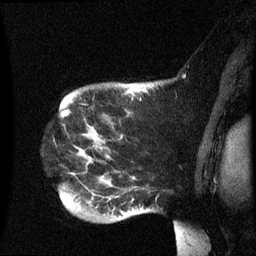
Breast MRI (dynamic contrast-enhanced), one sagittal slice; position 52 of 60 along the scan axis; dynamic contrast-enhanced series, image 2 of 3 at this slice position (ordered by acquisition); 1.5 T; TE 4.2 ms, TR 8.4 ms; 256 × 256 image matrix, field of view 220 × 220 mm. Female patient, age 49 years.
Outlined on this slice (semi-automatically segmented with operator editing):
- analysis volume of interest (the breast-tissue region the enhancement analysis was run in; not a lesion): bounding box [x1, y1, x2, y2] px = [61, 84, 185, 235]
- tumour enhancement mask (voxels above the 70 % enhancement threshold inside the analysis volume of interest): [67, 90, 133, 213]